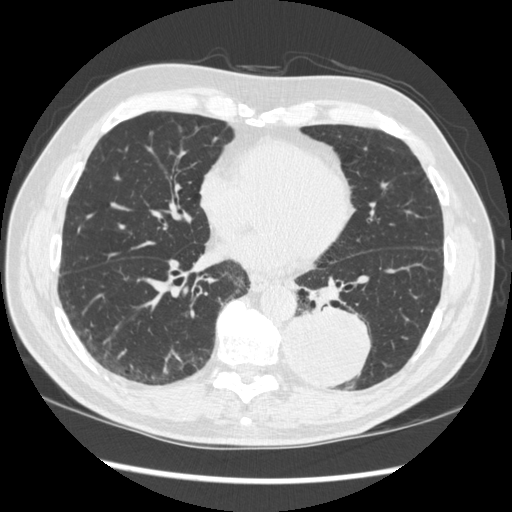
Low-dose screening chest CT, one axial slice; position 134 of 348 along the scan axis; 120 kVp; lung window (W 1500 / L -600 HU); 1.25 mm slice thickness; 512 × 512 image matrix, field of view 360 × 360 mm.
Annotated regions visible in this slice (outlined manually by an expert reader):
- lesion 1 (tumor, lower lobe of left lung): bounding box [x1, y1, x2, y2] px = [283, 309, 370, 388]